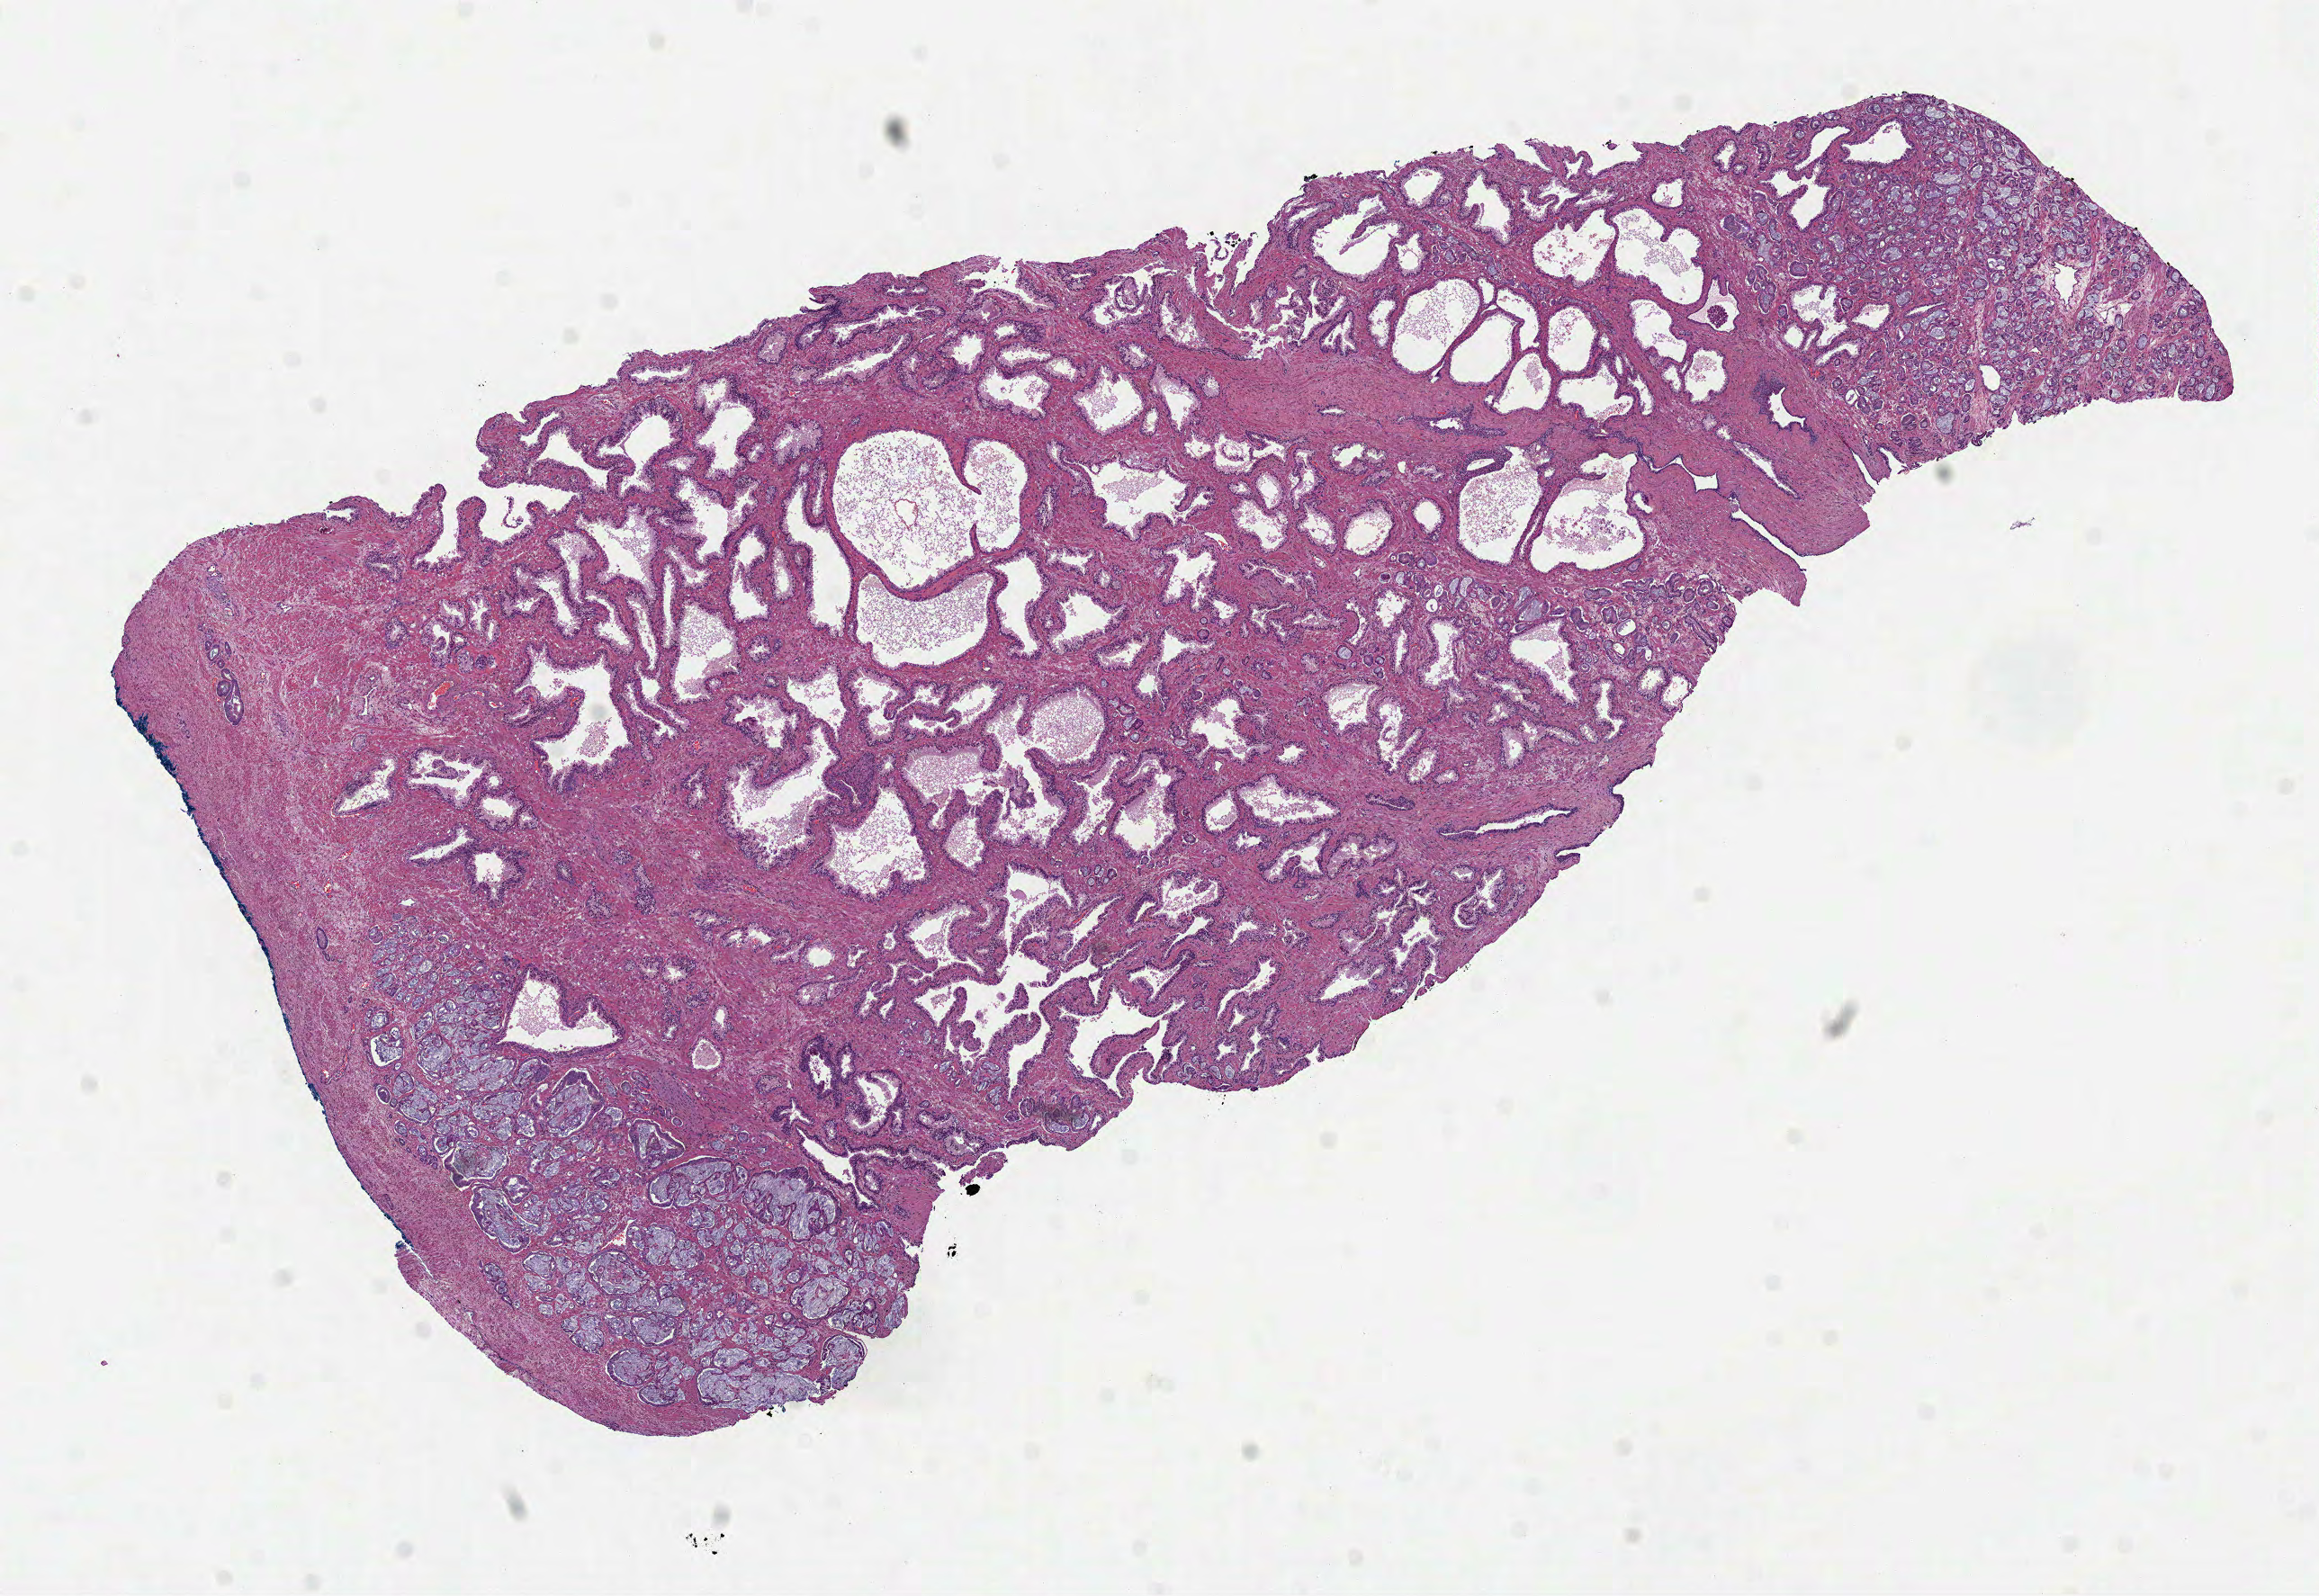
H&E-stained whole-slide image, shown as a low-resolution overview of the whole scanned area (about 10.4 x 7.2 mm, slide scanned at 40x), formalin-fixed paraffin-embedded (FFPE) diagnostic section, sample: primary tumour, prostate. Male, age 53 years at initial diagnosis. Gleason score: 8 (4+4).
Lymph nodes positive (case pathology): 0 of 3 examined. Diagnosis: Acinar cell carcinoma (prostate gland).